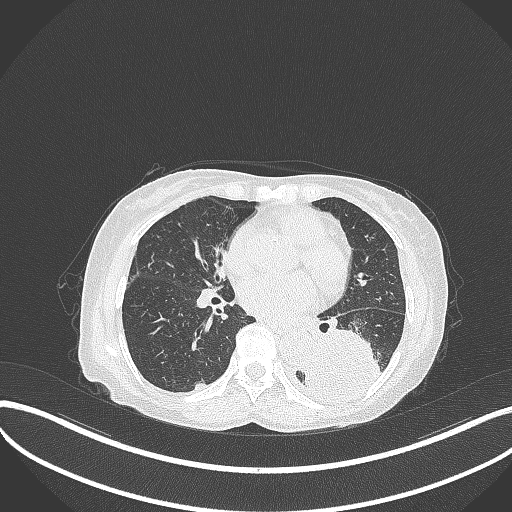
Chest CT, one axial slice. Slice 141 of 370 in the series (ordered by position). Reconstruction kernel B70f. 120 kVp. Lung window (W 1500 / L -600 HU). 1 mm slice thickness. 512 × 512 image matrix, field of view 400 × 400 mm. Female patient, age 78 years. Case-level facts recorded for this patient, not image findings: clinical TNM (as recorded): T3 N0 M1.
Annotated regions visible in this slice (rectangle marked by the reading radiologist):
- lung tumour (recorded histology: squamous cell carcinoma): bounding box <306,324,386,411> (left, top, right, bottom; pixels)